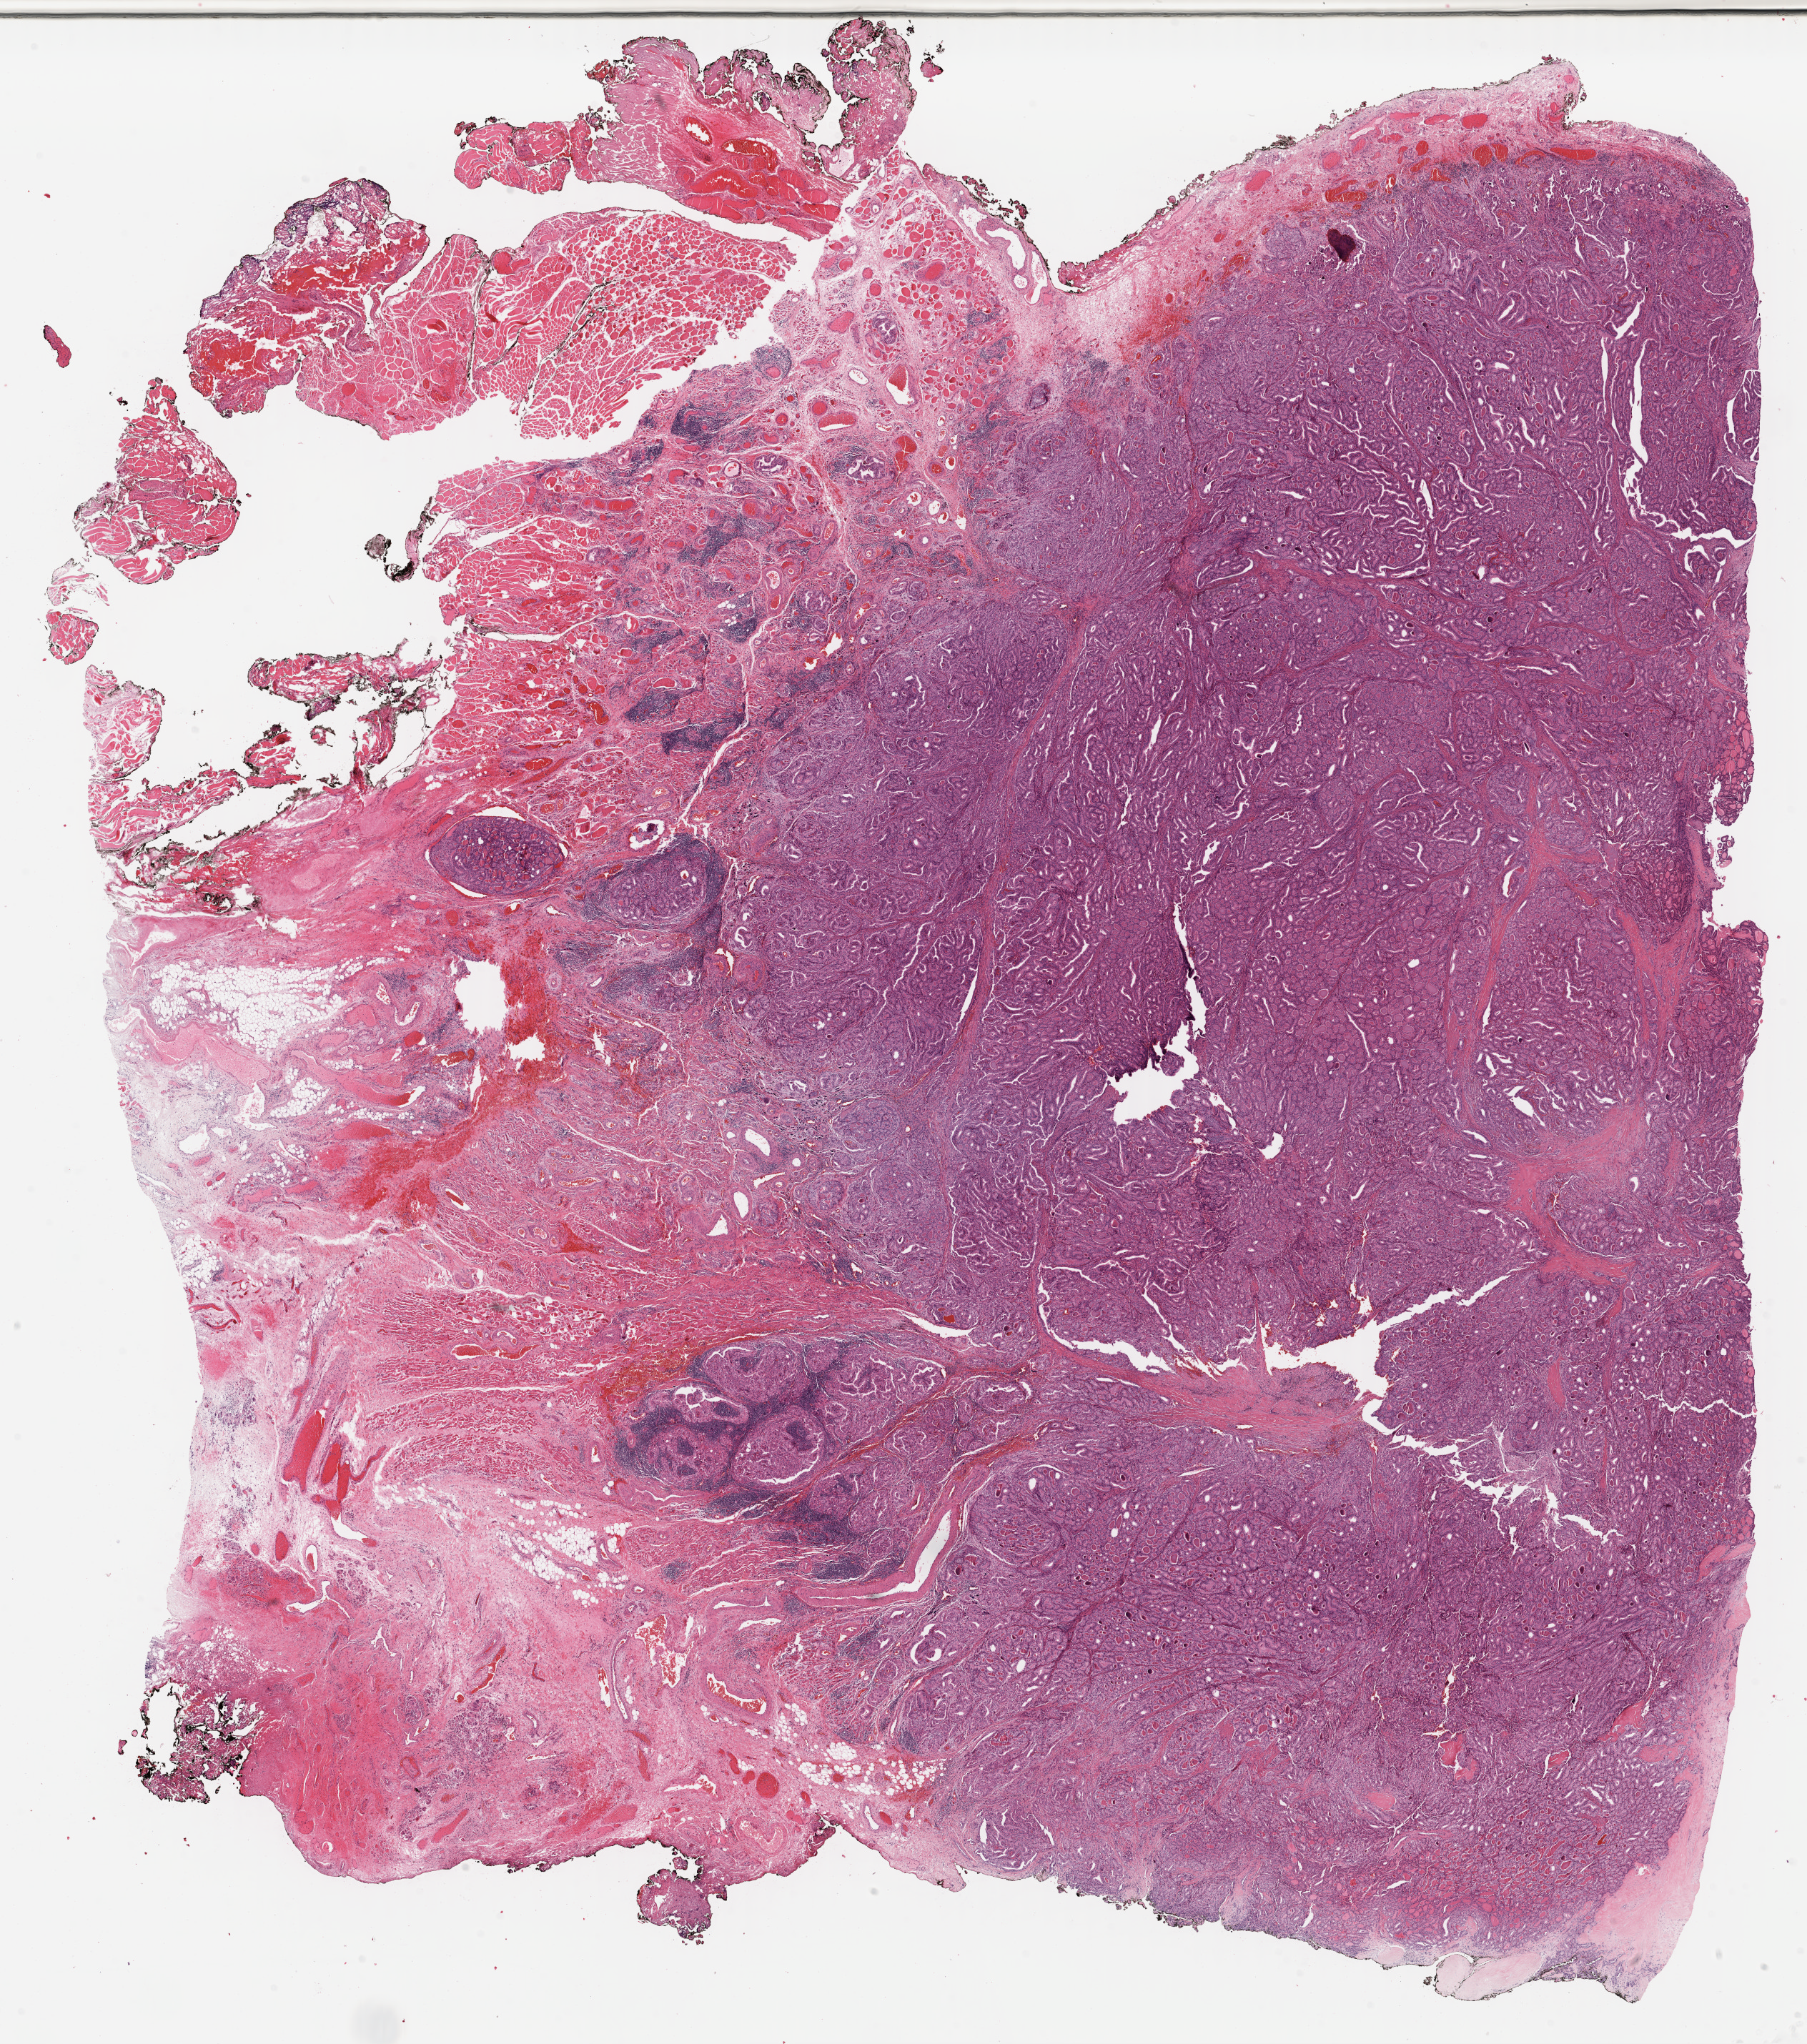
Whole-slide histology image, H&E-stained — a low-resolution overview of the entire scanned area, about 19.9 x 22.5 mm. FFPE section. Primary tumour sample from the thyroid. Female patient; age at initial diagnosis 61 years.
Lymph nodes positive (case pathology): 5 of 6 examined. Diagnosis: Papillary carcinoma, follicular variant (thyroid gland). AJCC pathologic stage: IVA.